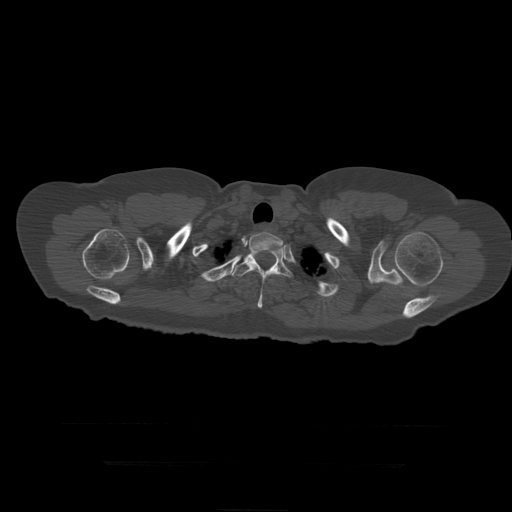
CT including the spine, one axial slice. Position 367 of 399 along the scan axis. Reconstruction kernel STANDARD. 120 kVp. Bone window (W 1800 / L 400 HU). 512 × 512 image matrix. Patient age 41 years. From the clinical record (not read from this slice): primary cancer: breast.
Outlined on this slice (semi-automatic segmentation, software-assisted and operator-edited):
- T2 vertebra: bounding box (x1, y1, x2, y2) in pixels: (246, 232, 284, 271)
- T3 vertebra: (231, 249, 294, 308)